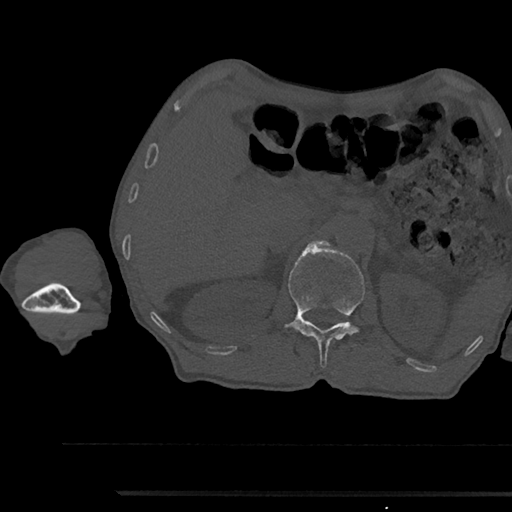
CT including the spine, one axial slice. Slice 636 of 797 in the series (ordered by position). 120 kVp. Bone window (W 1800 / L 400 HU). 0.5 mm slice thickness. 512 × 512 image matrix, field of view 367 × 367 mm. Patient: male, 79 years. From the clinical record (not read from this slice): primary cancer: prostate.
Annotated regions visible in this slice (semi-automatic segmentation, software-assisted and operator-edited):
- L1 vertebra: box from (x=288, y=241) to (x=365, y=368) px